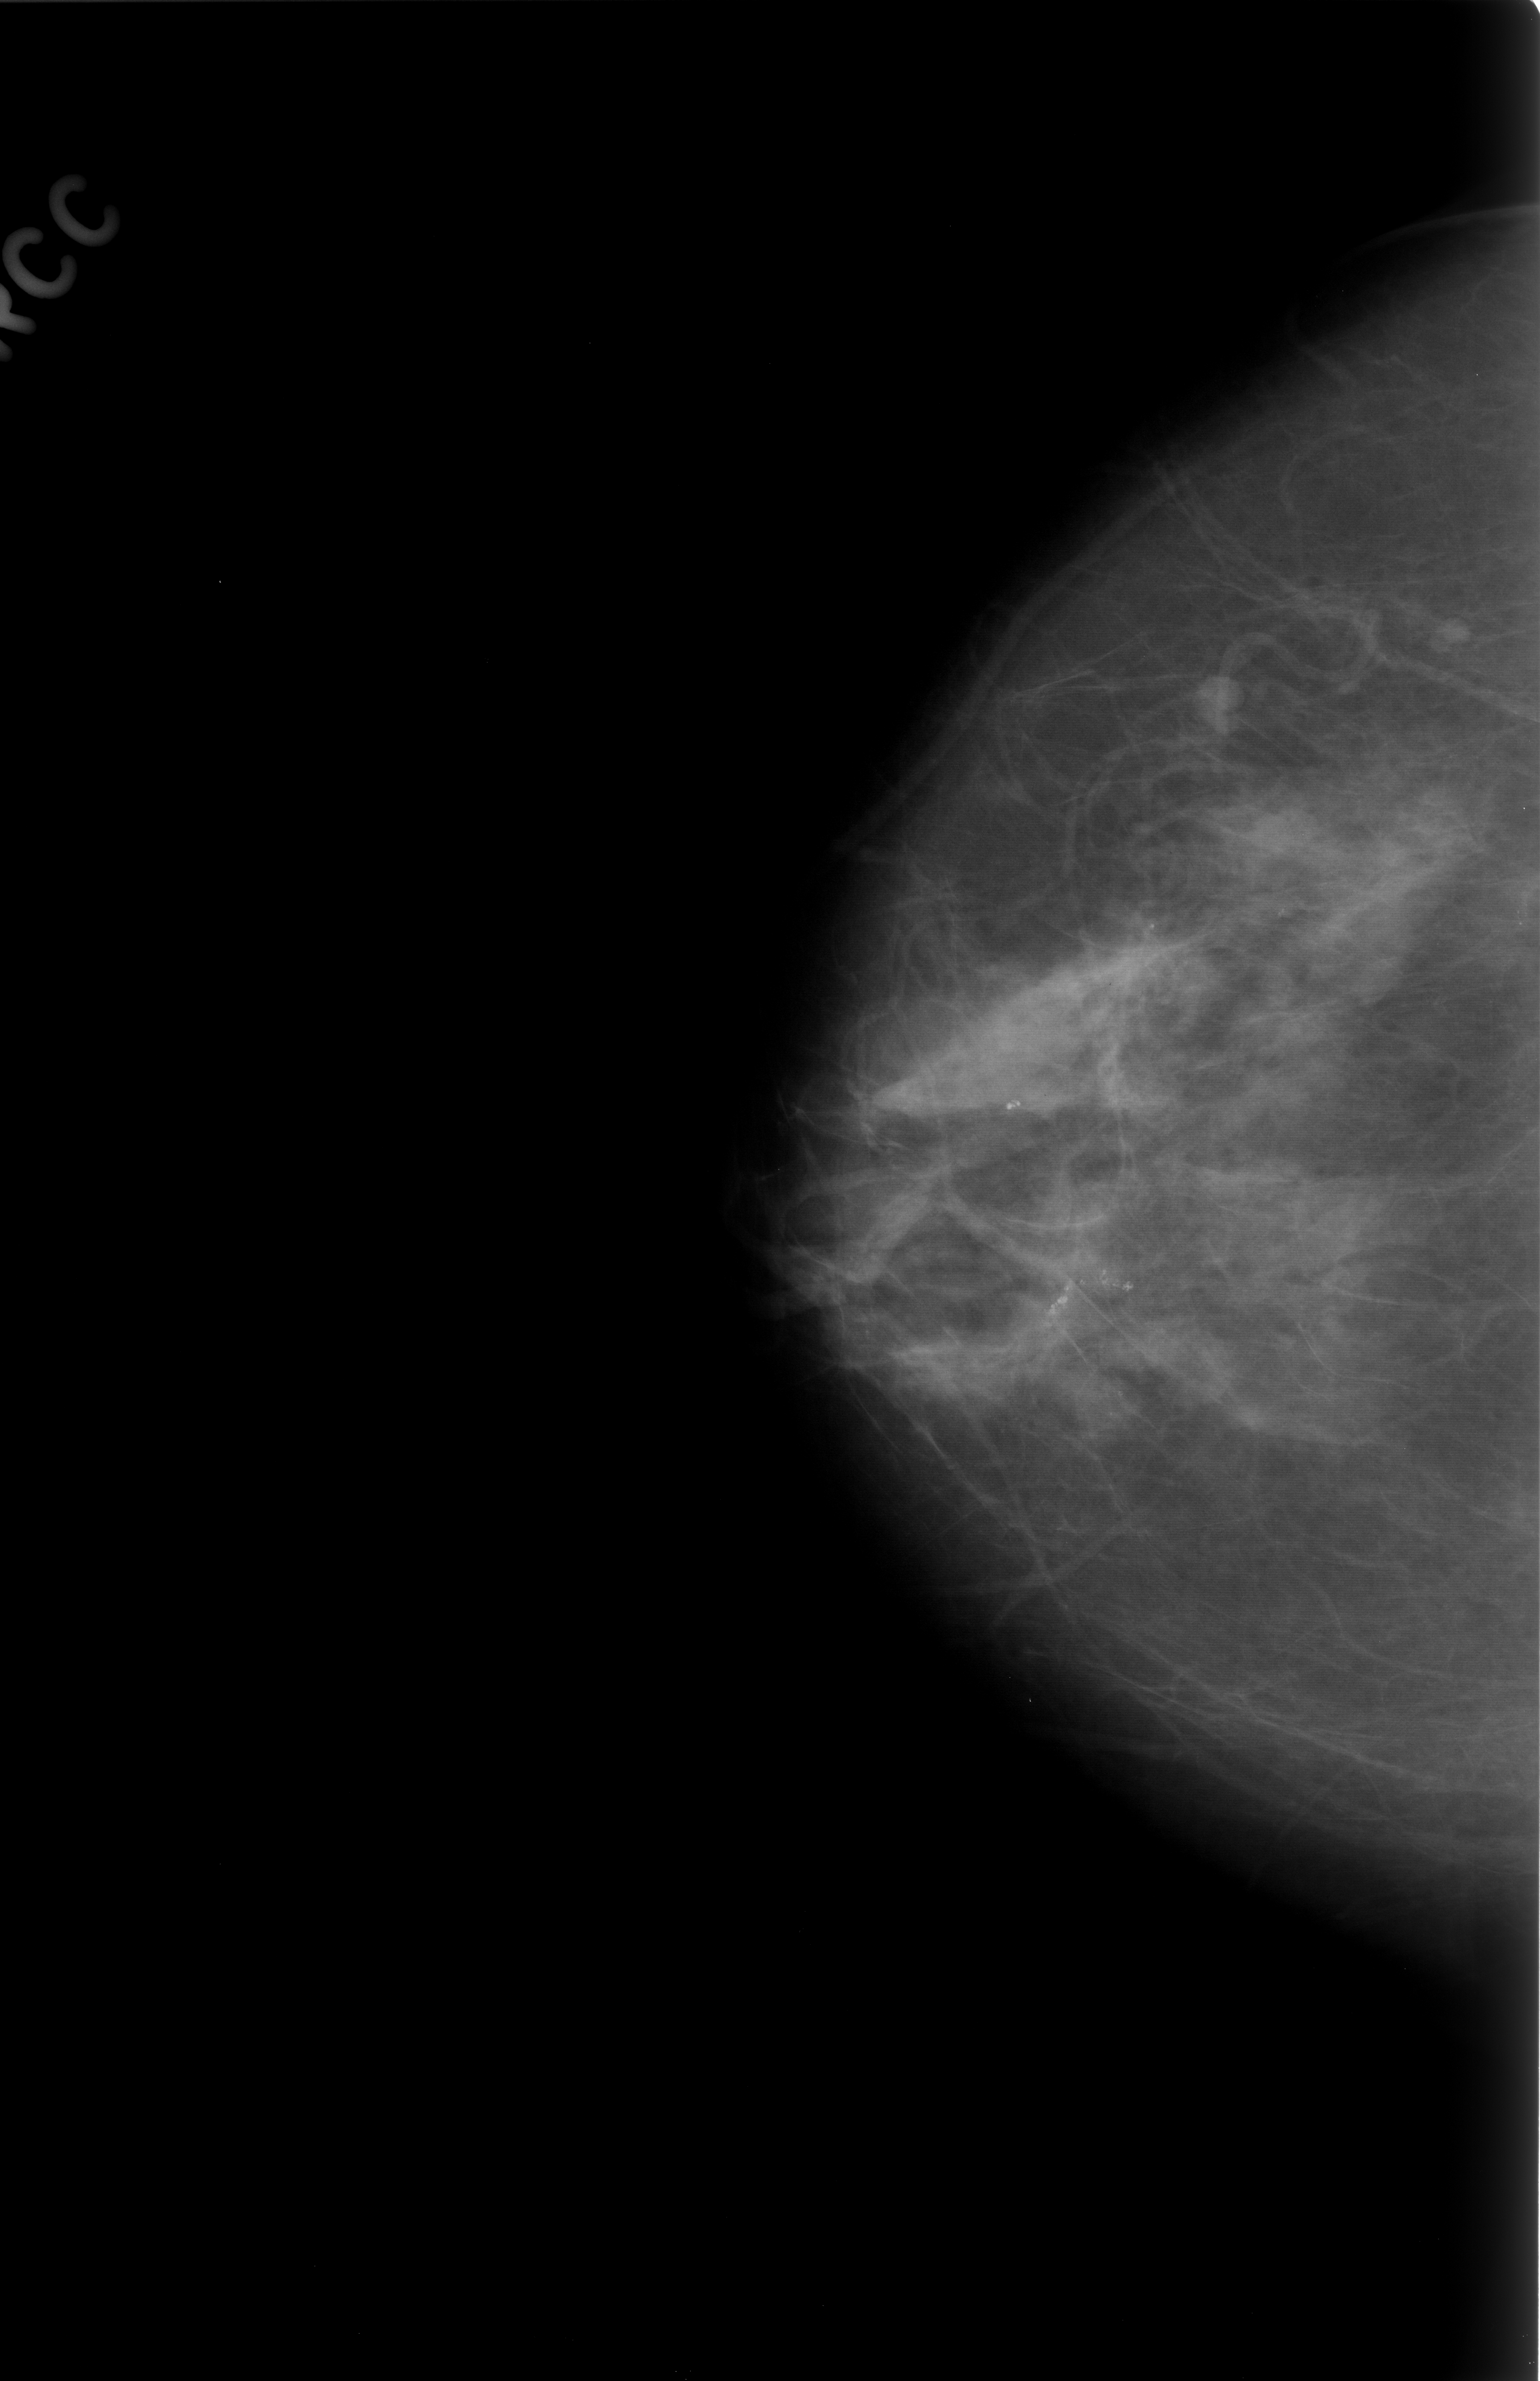
Mammogram (digitized film); right breast; craniocaudal (CC) view; breast composition: scattered fibroglandular densities (BI-RADS density category 2 of 4).
Marked abnormality: mass, shape lobulated, margins circumscribed; BI-RADS assessment category 2; subtlety rating 5 on a 1 (subtle) to 5 (obvious) scale; benign without callback (not worked up further).